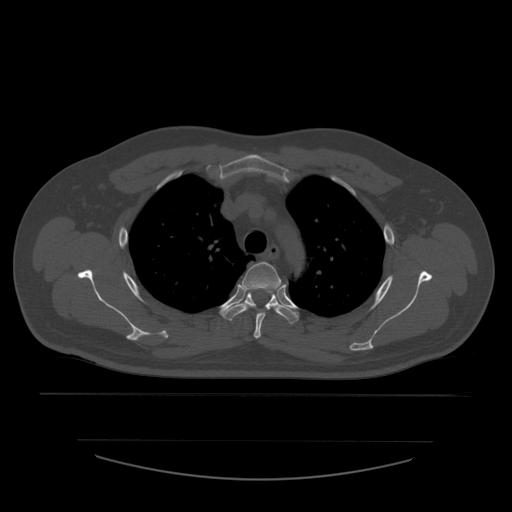
CT including the spine, one axial slice; slice 425 of 532 in the series (ordered by position); reconstruction kernel STANDARD; 120 kVp; bone window (W 1800 / L 400 HU); 512 × 512 image matrix, field of view 441 × 441 mm. Patient age 44 years. From the clinical record (not read from this slice): primary cancer: soft tissue sarcoma.
Outlined on this slice (semi-automatically segmented with operator editing):
- T3 vertebra: bounding box (x1, y1, x2, y2) in pixels: (241, 262, 284, 339)
- T4 vertebra: (222, 291, 299, 324)